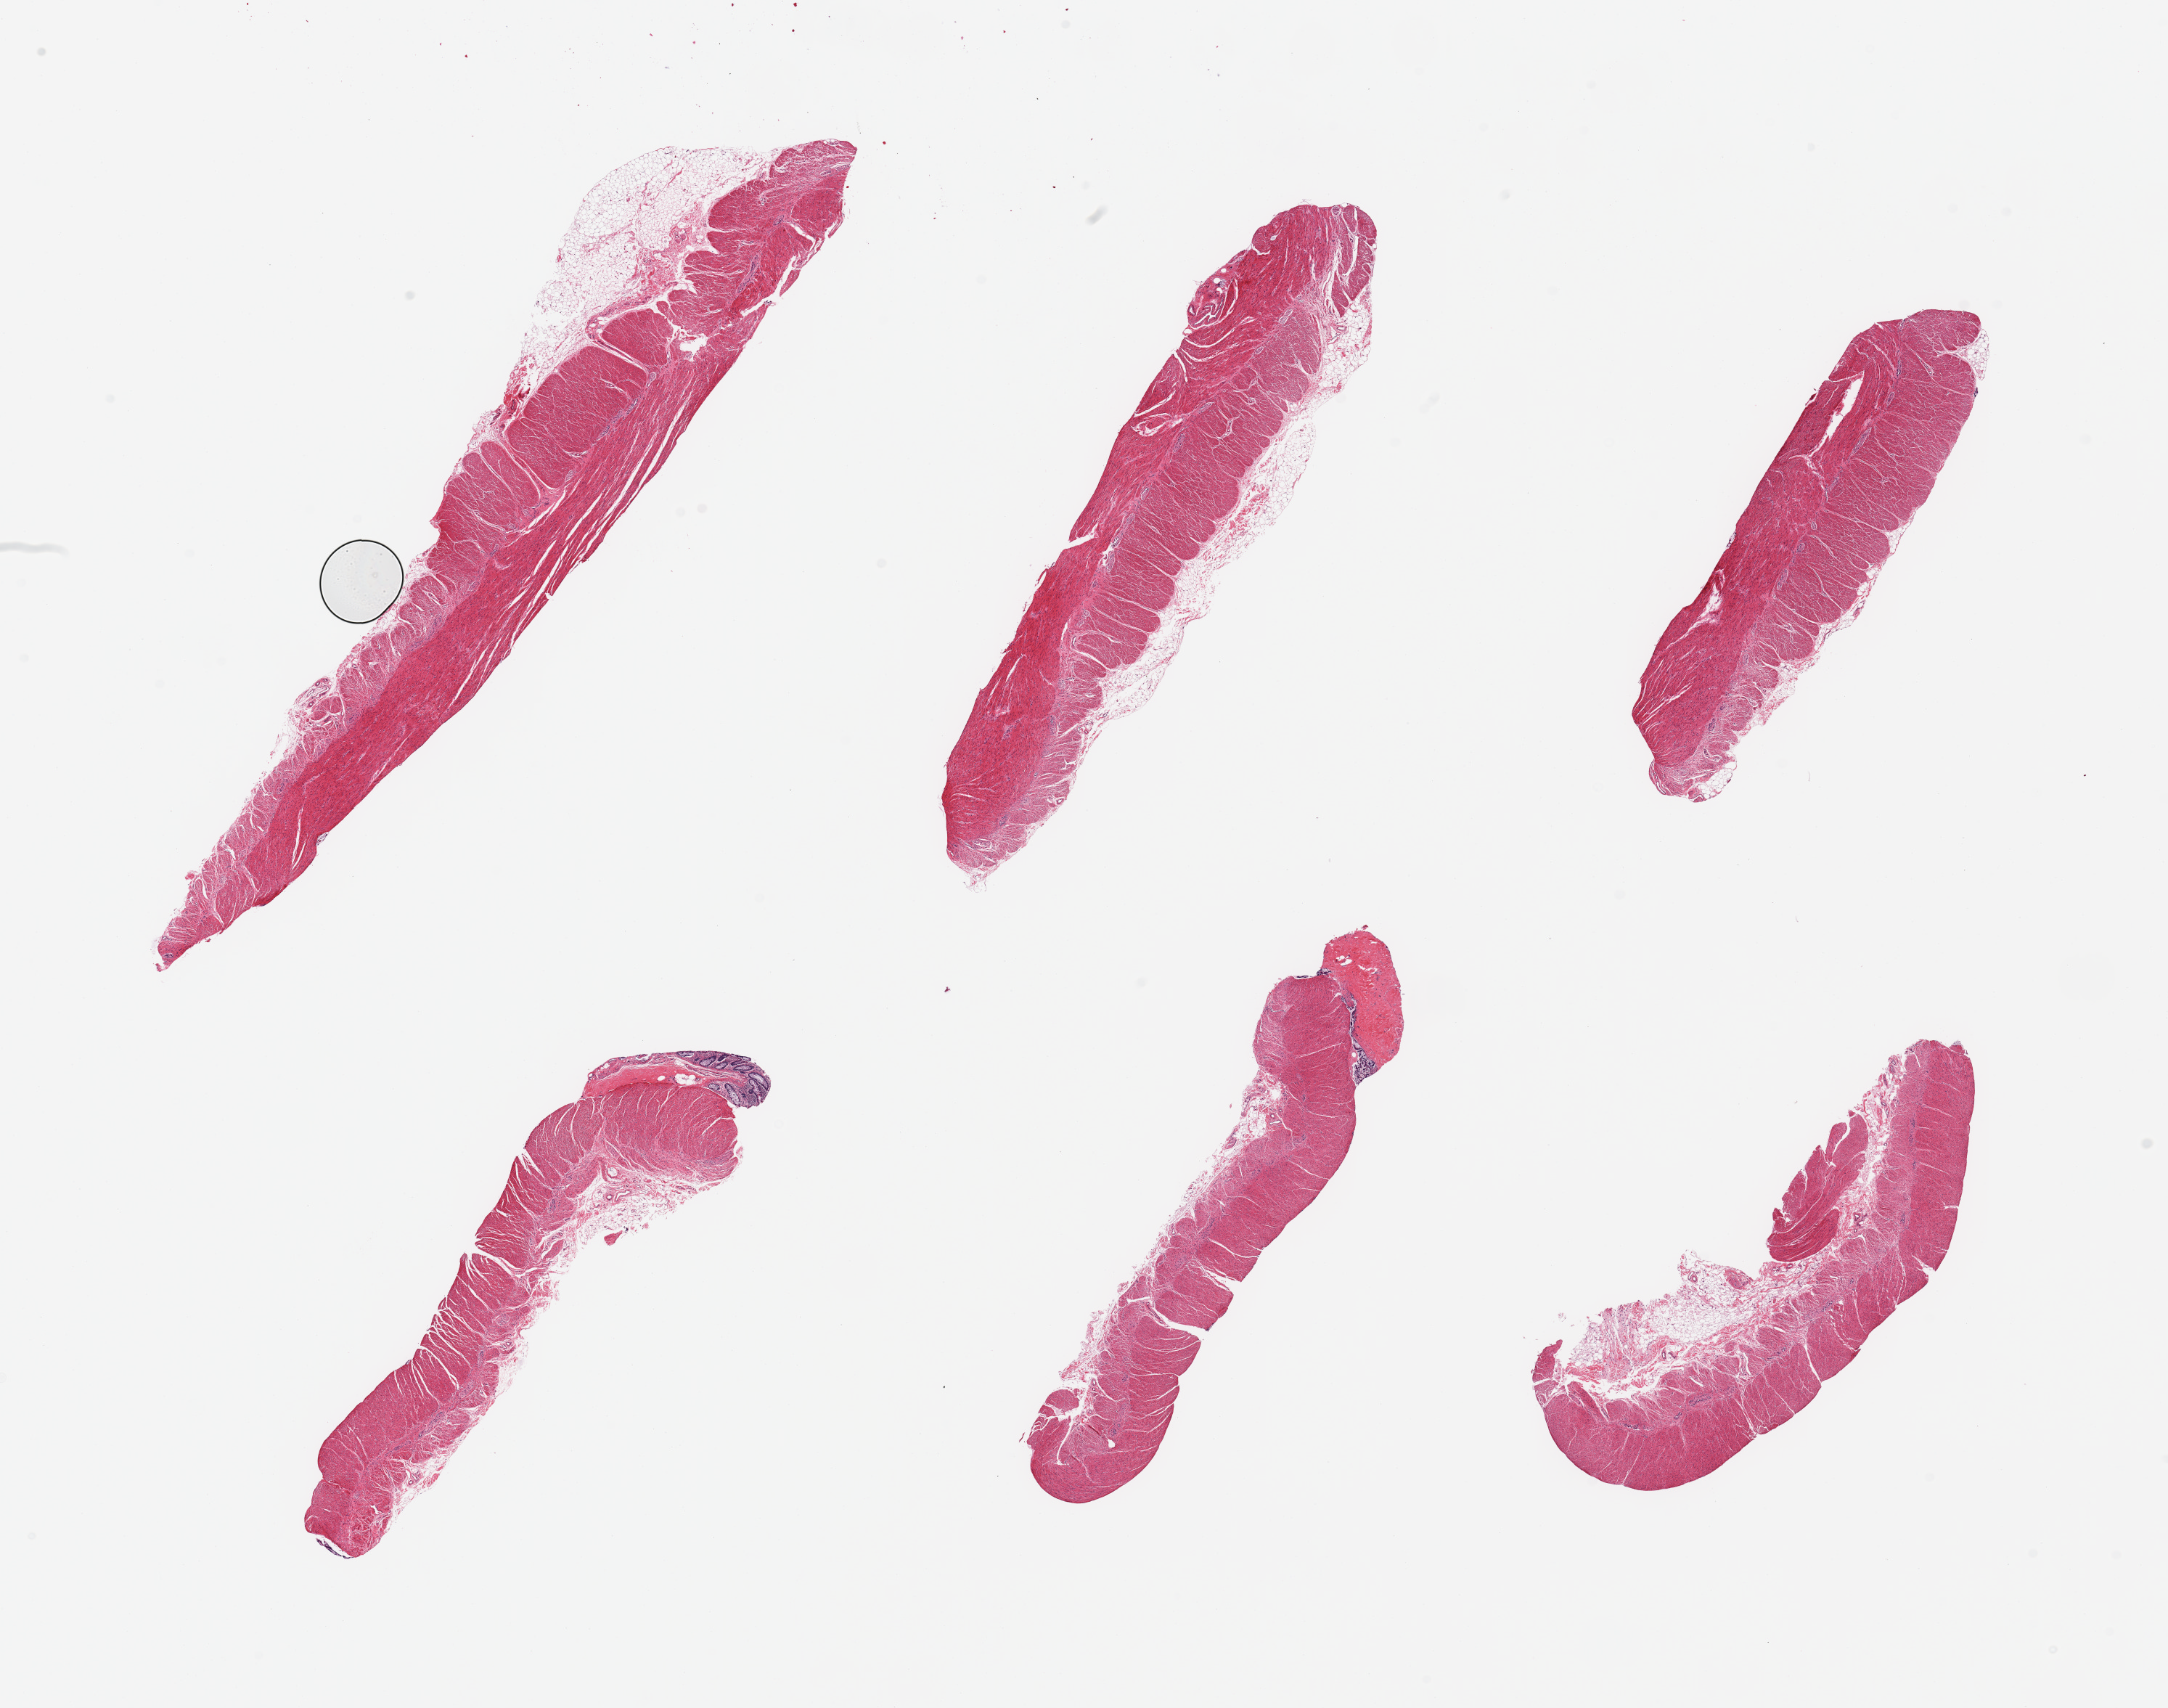
Digitized haematoxylin and eosin-stained section — whole scanned area (about 23.6 x 18.6 mm, slide scanned at 20x) shown as a low-resolution overview; PAXgene-fixed paraffin-embedded (PFPE) section; sampled site (target tissue): sigmoid colon; donor tissue sample.
Review note (as recorded): 6 pieces; muscularis with trace residual mucosa and attached fat.